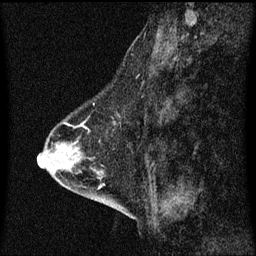
Breast MRI (dynamic contrast-enhanced), one sagittal slice. Slice 24 of 60 in the series (ordered by position). Dynamic contrast-enhanced series, image 2 of 3 at this slice position (ordered by acquisition). 1.5 T. TE 4.2 ms, TR 8.4 ms. 2 mm slice thickness. 256 × 256 image matrix, field of view 200 × 200 mm. Female patient, age 58 years.
Annotated regions visible in this slice (semi-automatic segmentation, software-assisted and operator-edited):
- analysis volume of interest (the breast-tissue region the enhancement analysis was run in; not a lesion): bounding box [x1, y1, x2, y2] px = [86, 100, 121, 143]
- tumour enhancement mask (voxels above the 70 % enhancement threshold inside the analysis volume of interest): [86, 128, 88, 131]